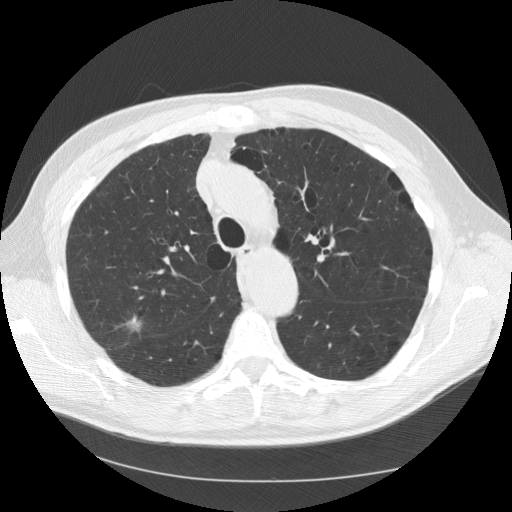
Low-dose screening chest CT, one axial slice; slice 93 of 133 in the series (ordered by position); reconstruction kernel STANDARD; 120 kVp; lung window (W 1500 / L -600 HU); 2.5 mm slice thickness; 512 × 512 image matrix.
Annotated regions visible in this slice (manually delineated by an expert):
- lesion 1 (tumor, upper lobe of right lung): bounding box [x1, y1, x2, y2] px = [126, 316, 141, 331]